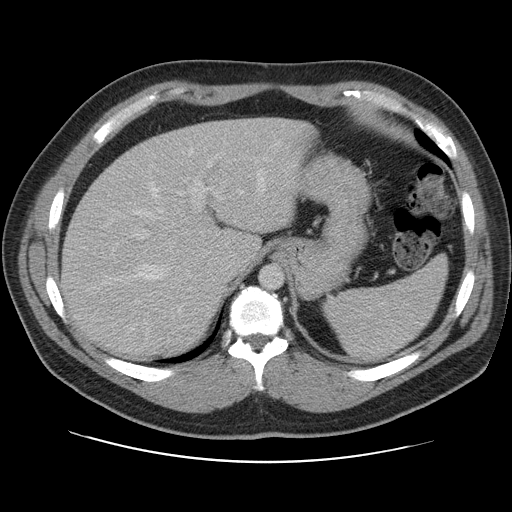
Contrast-enhanced abdominal CT, one axial slice. Position 82 of 109 along the scan axis. 120 kVp. Soft-tissue window (W 400 / L 40 HU). 5 mm slice thickness. 512 × 512 image matrix, field of view 402 × 402 mm. Male patient, age 35 years. Case-level facts recorded for this patient, not image findings: diagnosis: colorectal cancer liver metastases, imaged before liver resection; multiple liver metastases: yes; largest metastasis: 2.8 cm; disease in both lobes: yes.
Annotated regions visible in this slice (expert manual segmentation):
- hepatic veins: box from (x=115, y=157) to (x=268, y=281) px
- liver: (x=63, y=118)–(x=310, y=358)
- planned liver remnant (the part of the liver to remain after resection): (x=63, y=118)–(x=297, y=356)
- portal vein (with intrahepatic branches): (x=115, y=160)–(x=220, y=304)